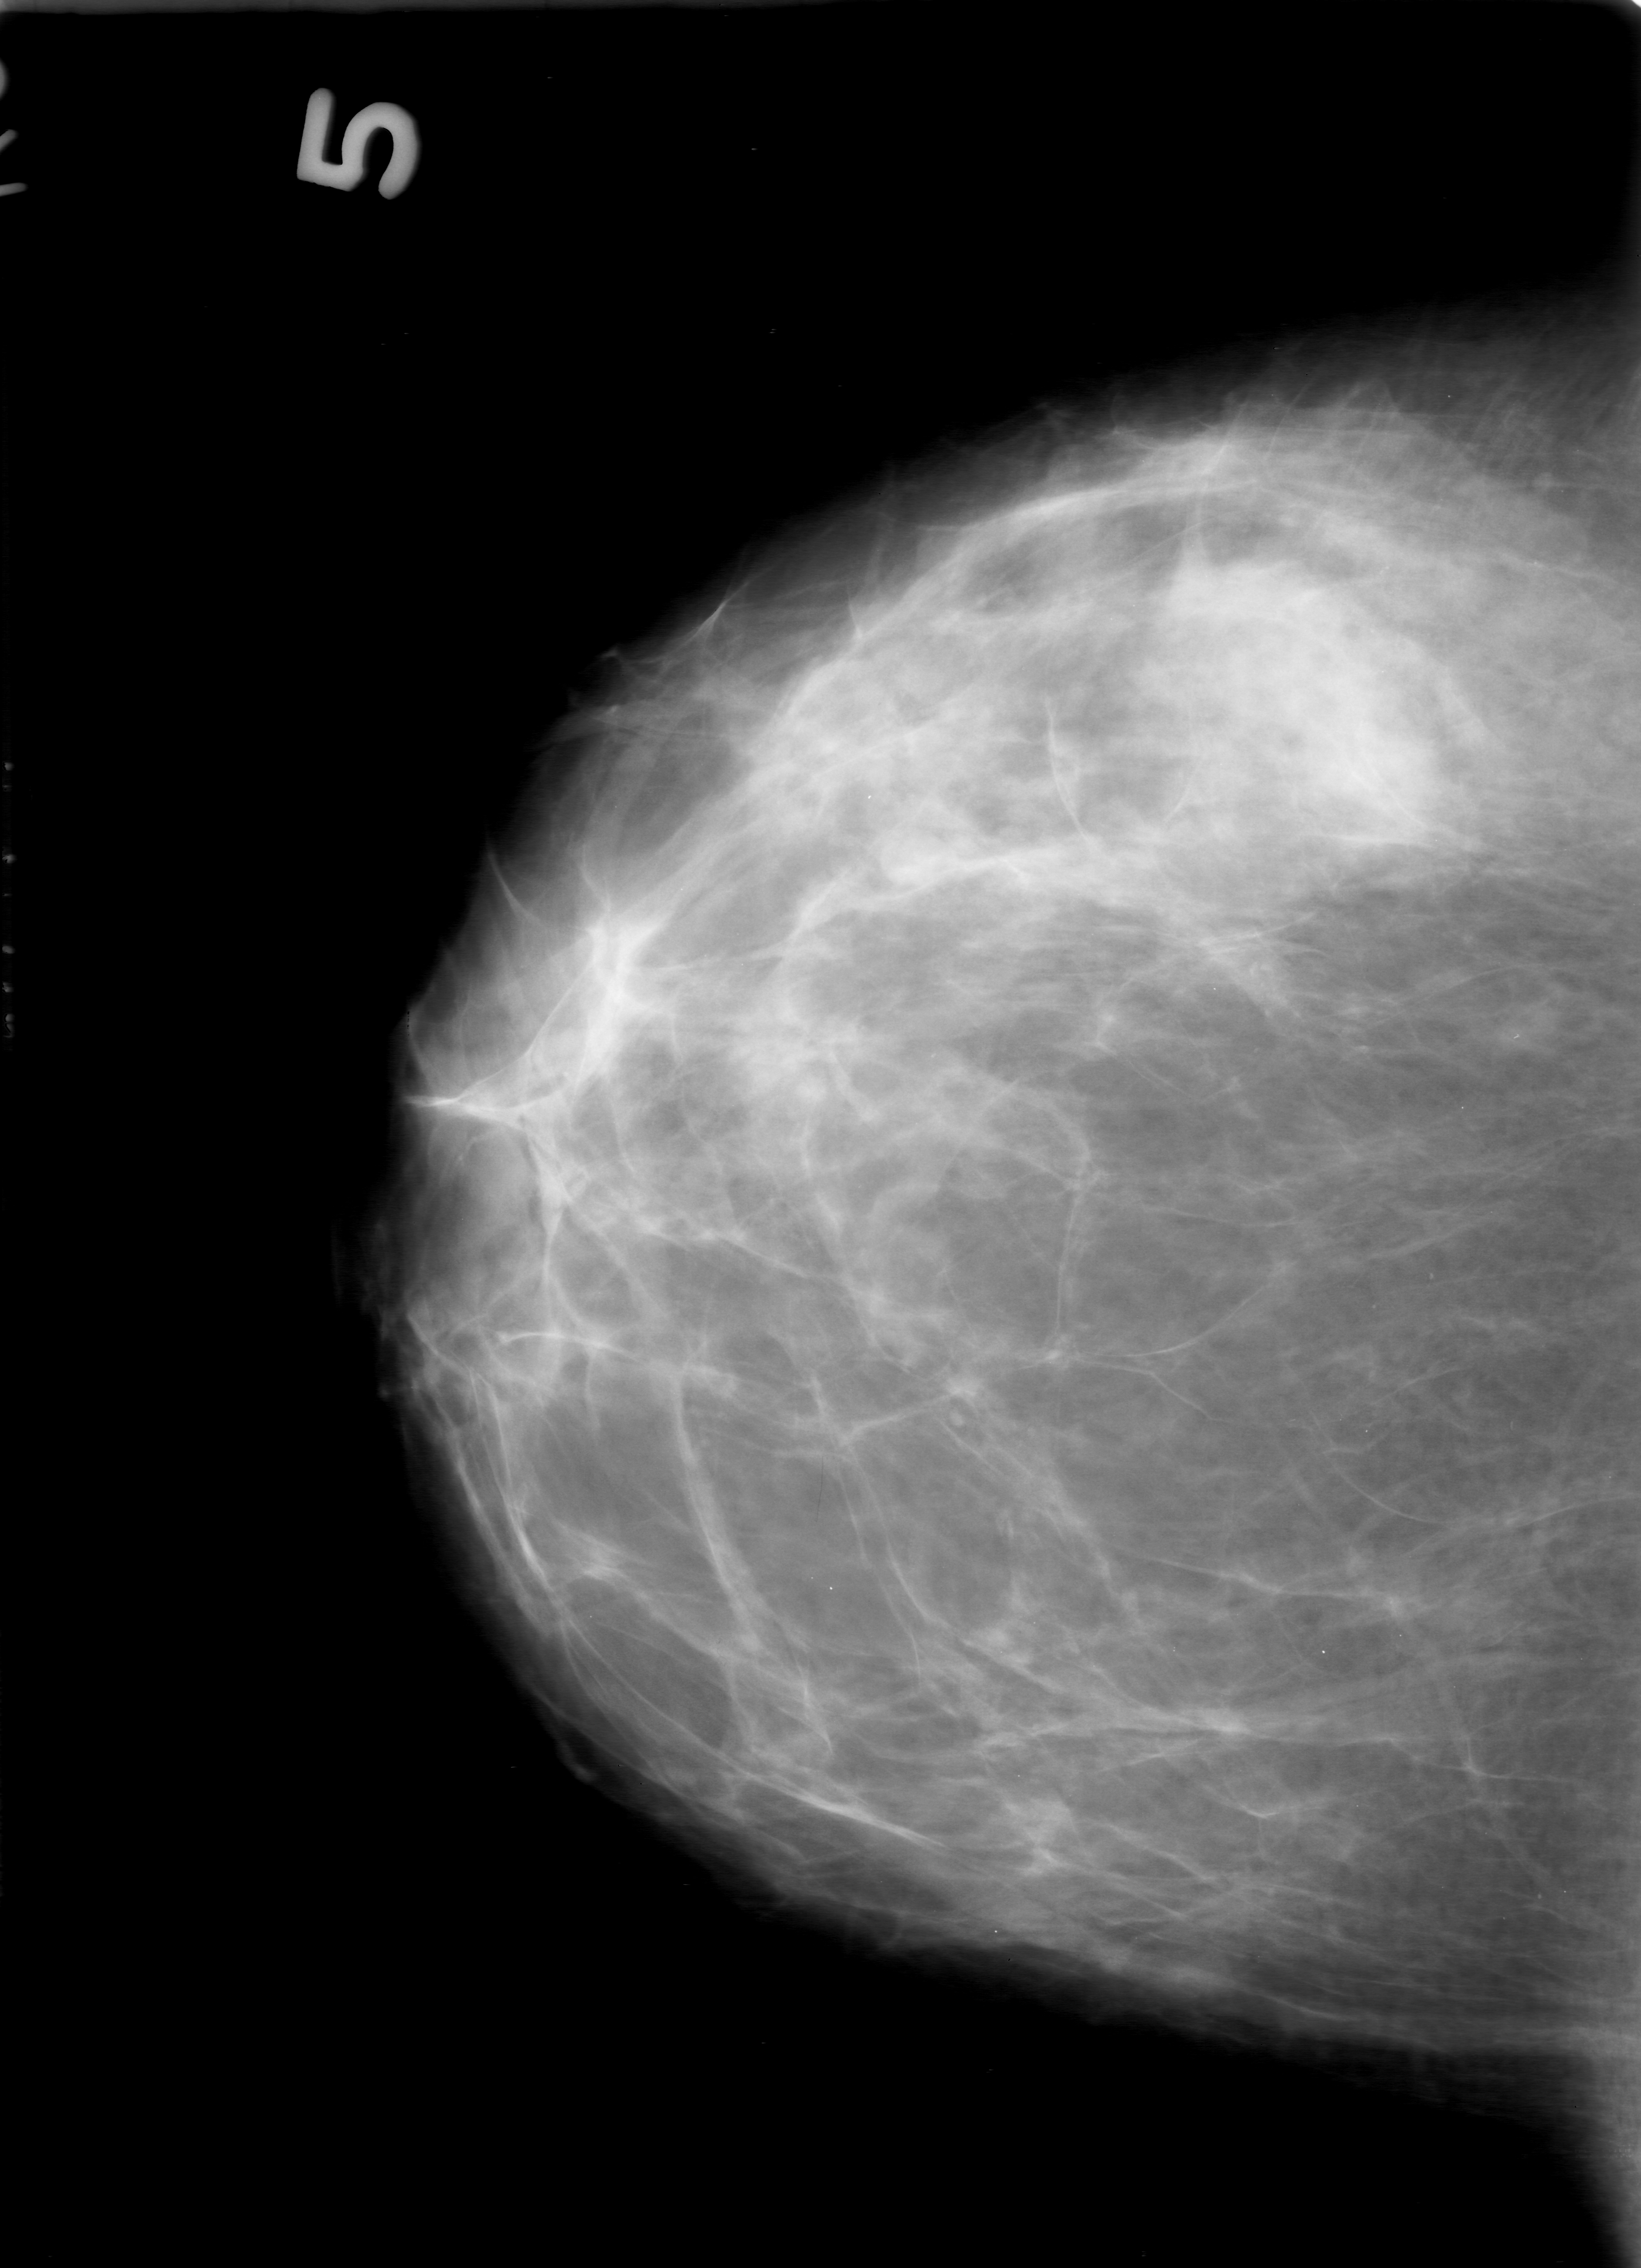
Digitized screen-film mammogram, right breast, CC view, breast composition: heterogeneously dense (BI-RADS density category 3 of 4).
Abnormality record for this image: calcifications, morphology punctate / amorphous, distribution clustered; BI-RADS assessment category 0; pathology (as recorded): benign.